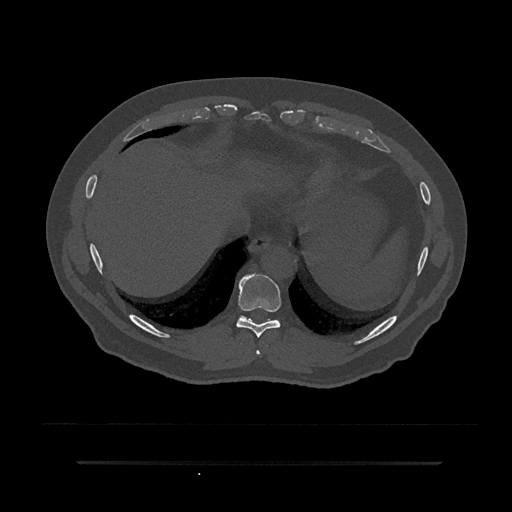
CT including the spine, one axial slice; position 369 of 797 along the scan axis; reconstruction kernel Br40s/3; 120 kVp; bone window (W 1800 / L 400 HU); 0.5 mm slice thickness; 512 × 512 image matrix. Patient: male, 59 years. Case-level facts recorded for this patient, not image findings: primary cancer: bile ducts.
Annotated regions visible in this slice (semi-automatically segmented with operator editing):
- T8 vertebra: bounding box [x1, y1, x2, y2] px = [256, 350, 261, 355]
- T9 vertebra: [236, 274, 281, 338]